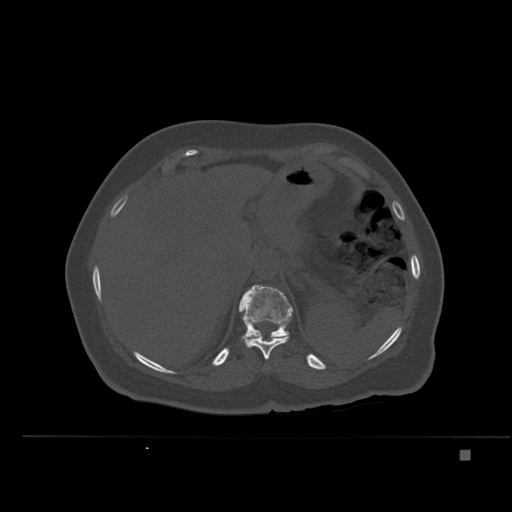
CT including the spine, one axial slice; slice 263 of 477 in the series (ordered by position); bone window (W 1800 / L 400 HU); 1.5 mm slice thickness; 512 × 512 image matrix. Female patient, age 74 years. Case-level facts recorded for this patient, not image findings: primary cancer: colon.
Annotated regions visible in this slice (semi-automatic segmentation, software-assisted and operator-edited):
- T11 vertebra: bounding box <244,335,289,360> (left, top, right, bottom; pixels)
- T12 vertebra: <238,285,293,340>